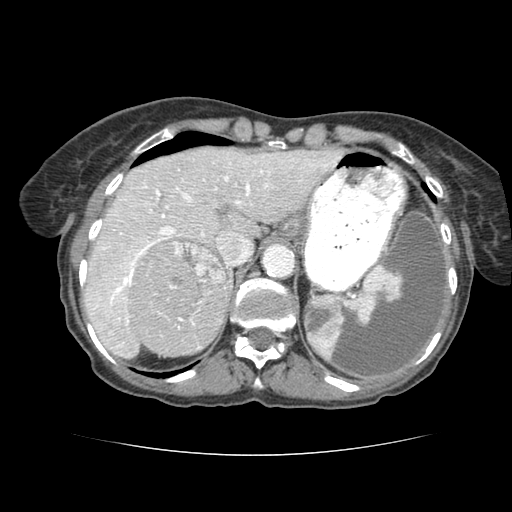
Contrast-enhanced abdominal CT (liver protocol), one axial slice. Slice 58 of 77 in the series (ordered by position). 120 kVp. Soft-tissue window (W 400 / L 40 HU). 512 × 512 image matrix, field of view 340 × 340 mm. From the clinical record (not read from this slice): diagnosis: hepatocellular carcinoma (patient treated with transarterial chemoembolisation; whether this scan precedes or follows treatment is not stated here); TNM stage (as recorded): Stage-I; Child-Pugh class: A; tumour differentiation: well differentiated; tumour size: 7.6 cm.
Annotated regions visible in this slice (semi-automatic segmentation, software-assisted and operator-edited):
- liver parenchyma outside the tumour (the mass and vessels are separate outlines, so this box may not span the whole liver): bounding box <80,146,330,352> (left, top, right, bottom; pixels)
- mass: <124,238,228,351>
- liver vessels: <80,167,240,301>